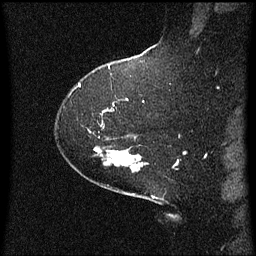
Breast MRI (dynamic contrast-enhanced), one sagittal slice. Position 45 of 60 along the scan axis. Dynamic contrast-enhanced series, image 2 of 3 at this slice position (ordered by acquisition). 1.5 T. TE 4.2 ms, TR 8 ms. 2.1 mm slice thickness. 256 × 256 image matrix, field of view 200 × 200 mm. Patient: female, 59 years.
Structures marked on this image (semi-automatically segmented with operator editing):
- analysis volume of interest (the breast-tissue region the enhancement analysis was run in; not a lesion): bounding box (x1, y1, x2, y2) in pixels: (94, 148, 143, 173)
- tumour enhancement mask (voxels above the 70 % enhancement threshold inside the analysis volume of interest): (130, 164, 139, 169)